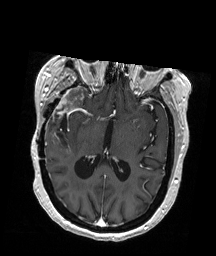
Brain MRI from a brain-tumour surgery series, one axial slice; position 103 of 192 along the scan axis; T1-weighted post-contrast; 1 mm slice thickness; 216 × 256 image matrix, field of view 211 × 250 mm. Case-level facts recorded for this patient, not image findings: histopathology: Glioblastoma; WHO grade: 4; IDH mutation: no; tumour location: Right Temporal.
Annotated regions visible in this slice (expert manual segmentation):
- tumour: bounding box [x1, y1, x2, y2] px = [50, 87, 87, 136]